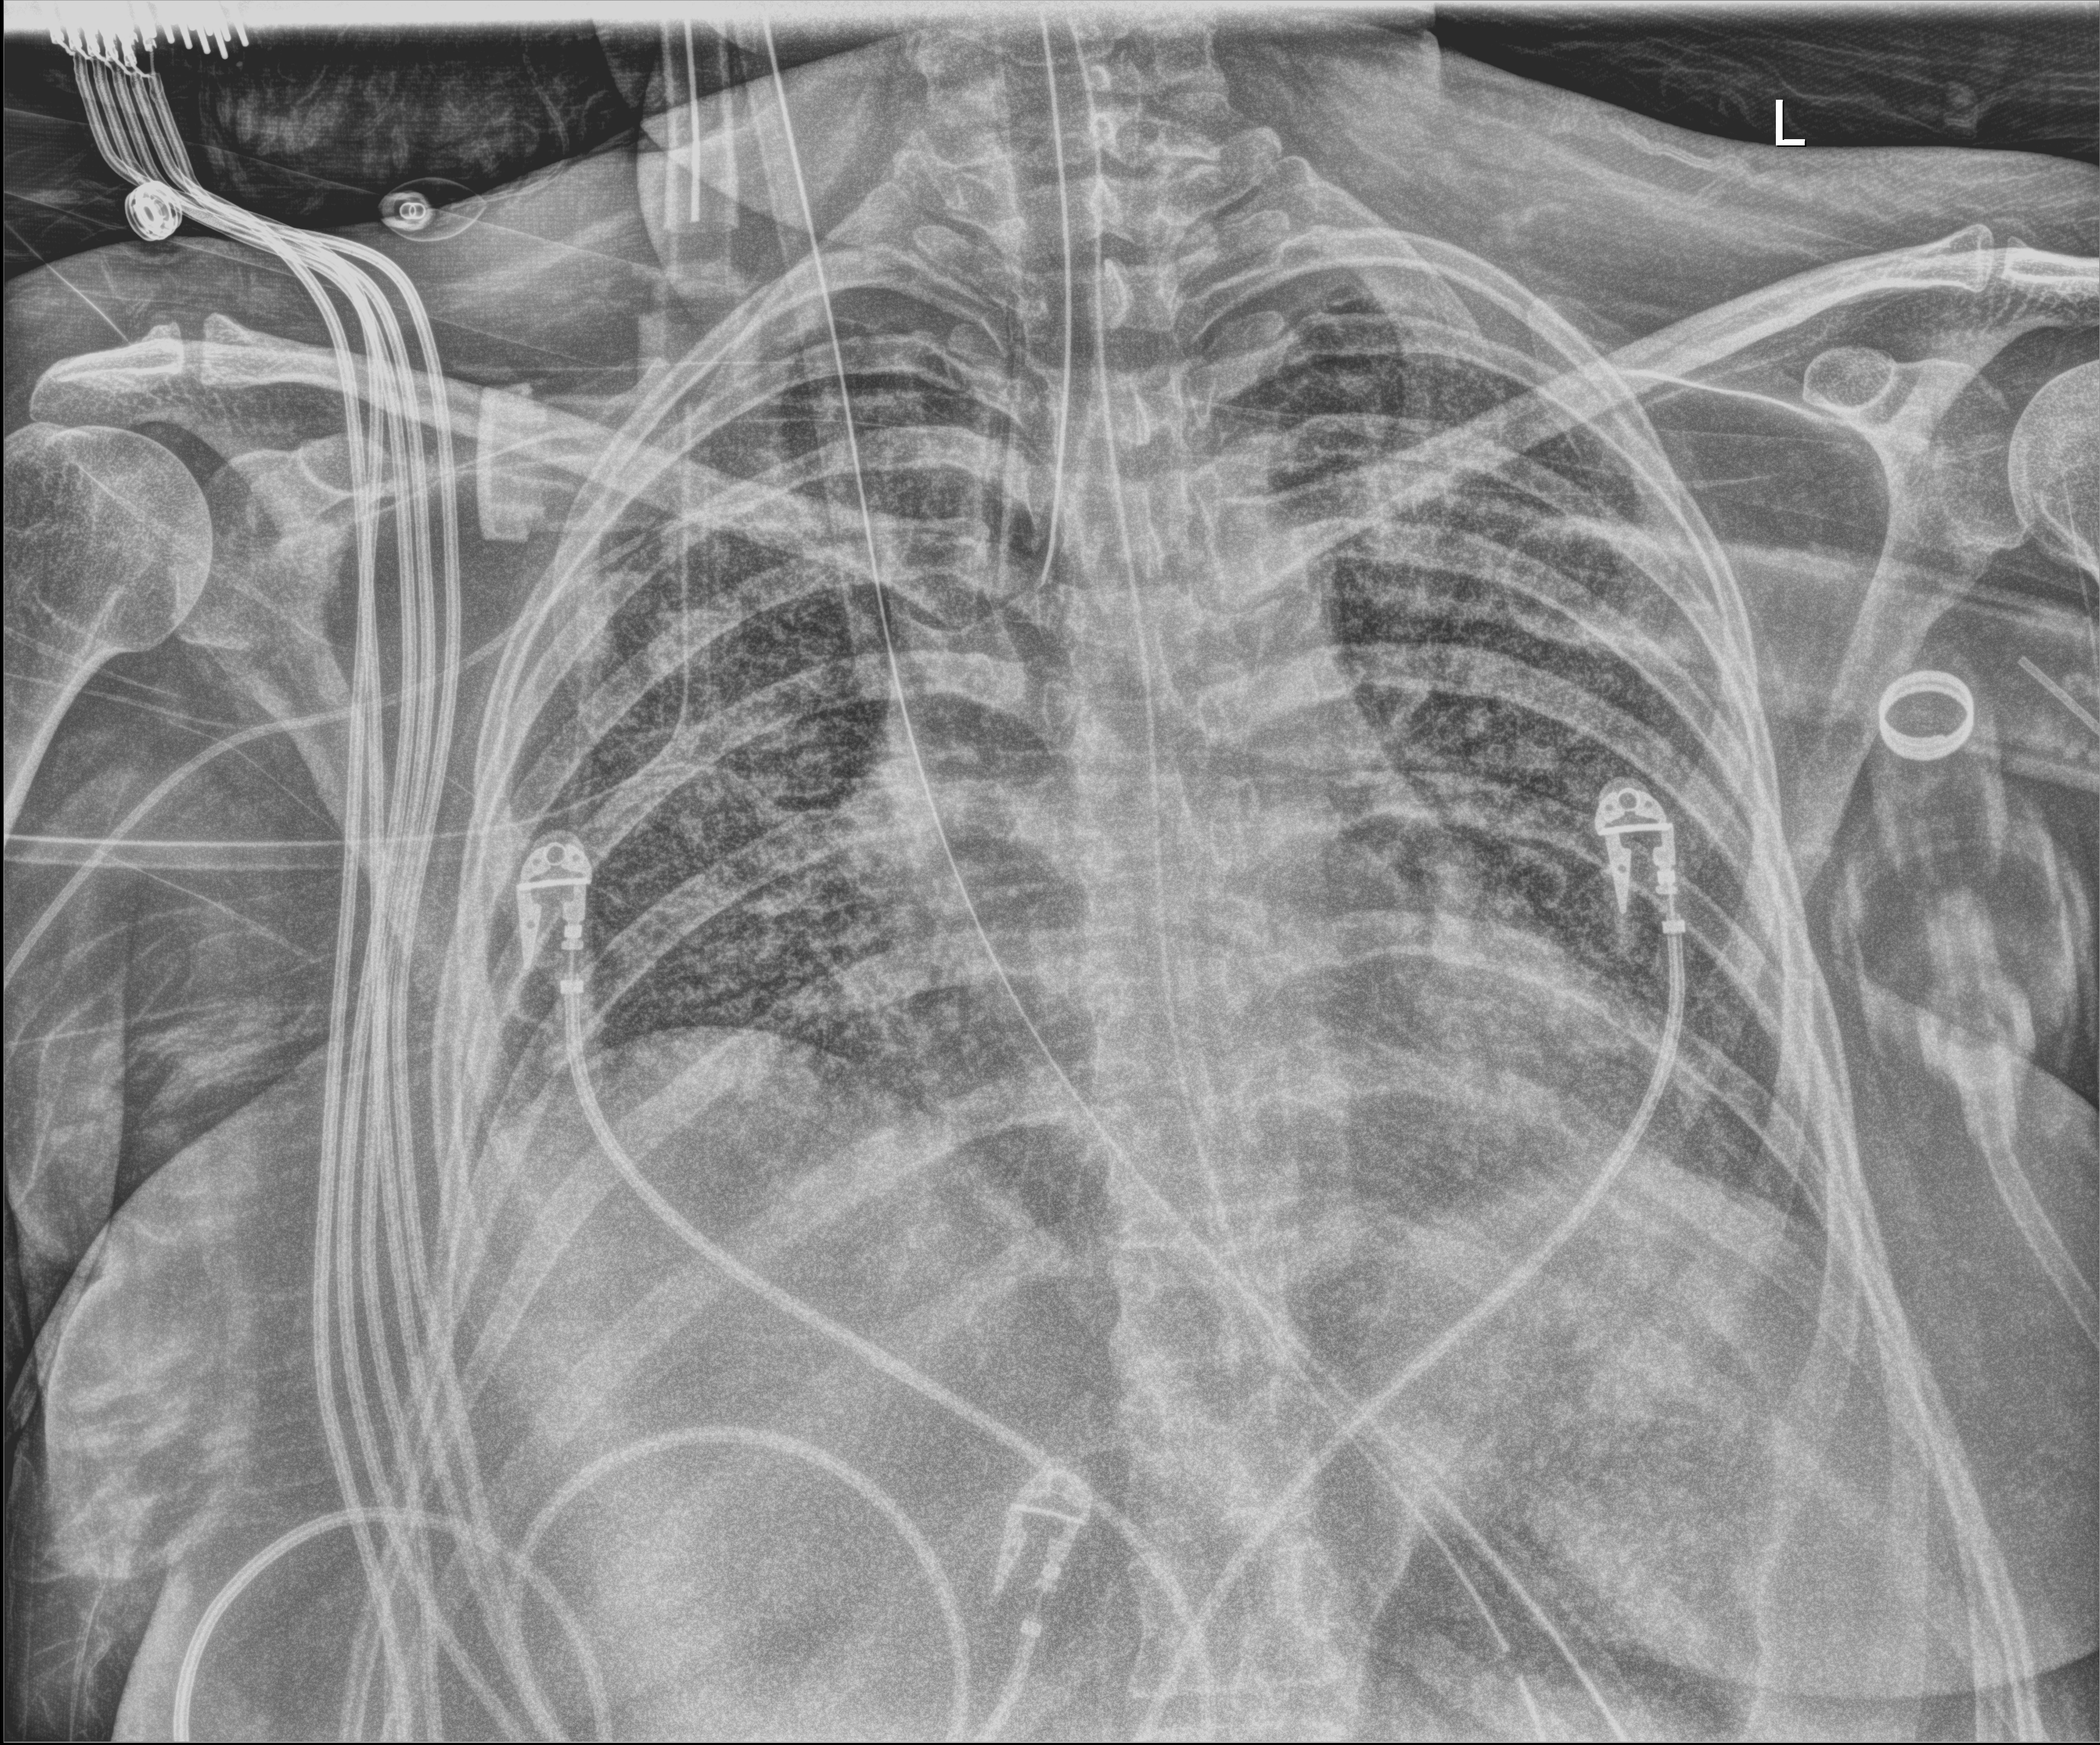
Portable chest radiograph, anteroposterior (AP) projection. Patient hospitalised with COVID-19; female, aged 18–59 years.
Hospital-stay facts (about this admission, not read from this image; timing relative to this image not recorded):
- mechanically ventilated during this hospital stay: yes
- other chronic lung disease (admission record): yes
- admitted to intensive care during this hospital stay: yes